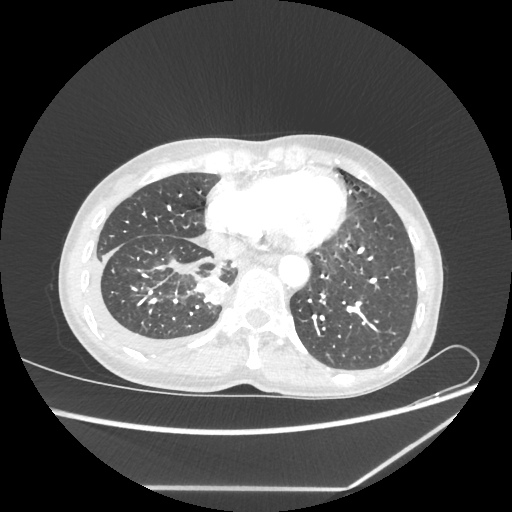
Chest CT, one axial slice. Position 65 of 237 along the scan axis. Reconstruction kernel STANDARD. Lung window (W 1500 / L -600 HU). 1.25 mm slice thickness. 512 × 512 image matrix, field of view 364 × 364 mm. Patient: female, 59 years. Case-level facts recorded for this patient, not image findings: clinical TNM (as recorded): T1c N1 M1.
Structures marked on this image (rectangle marked by the reading radiologist):
- lung tumour (recorded histology: adenocarcinoma): box from (x=191, y=272) to (x=230, y=305) px